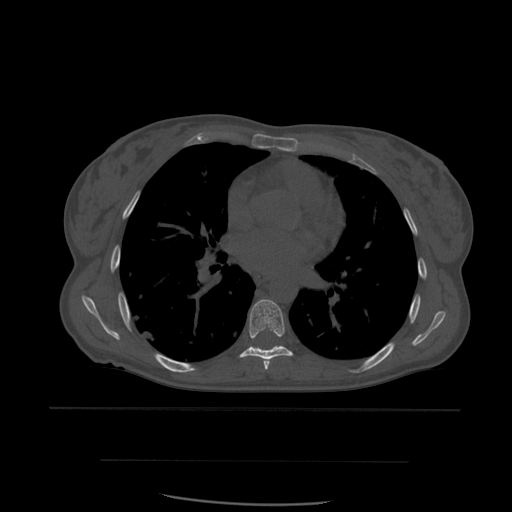
CT including the spine, one axial slice. Slice 375 of 574 in the series (ordered by position). Bone window (W 1800 / L 400 HU). 1.25 mm slice thickness. 512 × 512 image matrix, field of view 392 × 392 mm. Patient age 48 years. From the clinical record (not read from this slice): primary cancer: lung; vertebrae with lytic lesions (as recorded): T11.
Structures marked on this image (semi-automatically segmented with operator editing):
- T6 vertebra: bounding box <264,361,270,370> (left, top, right, bottom; pixels)
- T7 vertebra: <239,299,293,362>